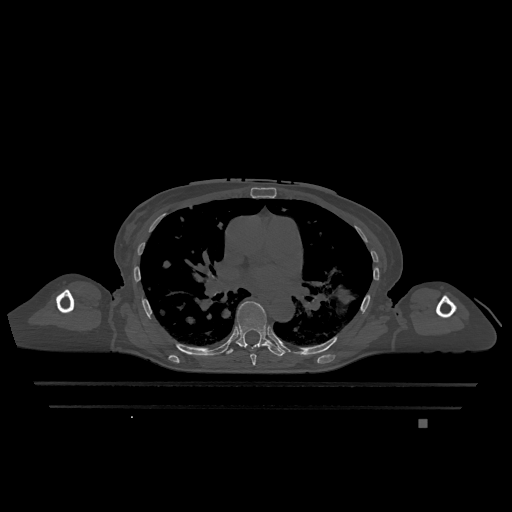
CT including the spine, one axial slice; slice 756 of 1317 in the series (ordered by position); bone window (W 1800 / L 400 HU); 512 × 512 image matrix, field of view 500 × 500 mm. Patient: female, 74 years. From the clinical record (not read from this slice): primary cancer: lung; vertebrae with lytic lesions (as recorded): T1, T4, T5, T6, L4, L5.
Structures marked on this image (semi-automatically segmented with operator editing):
- T6 vertebra: bounding box <250,354,256,366> (left, top, right, bottom; pixels)
- T7 vertebra: <223,301,286,357>